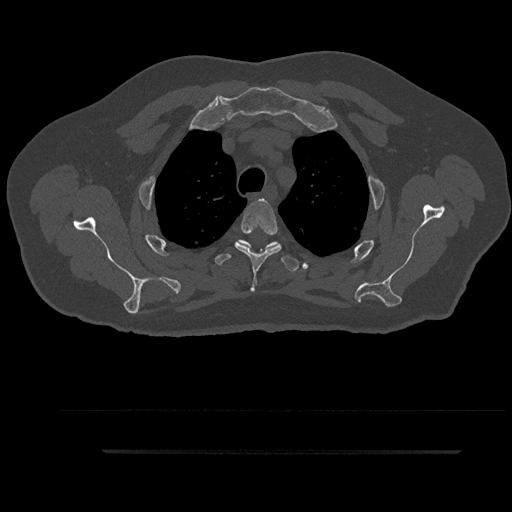
CT including the spine, one axial slice; slice 707 of 797 in the series (ordered by position); 120 kVp; bone window (W 1800 / L 400 HU); 512 × 512 image matrix, field of view 432 × 432 mm. Male patient, age 63 years. Case-level facts recorded for this patient, not image findings: primary cancer: renal; vertebrae with lytic lesions (as recorded): T8.
Annotated regions visible in this slice (semi-automatically segmented with operator editing):
- T3 vertebra: bounding box (x1, y1, x2, y2) in pixels: (235, 199, 281, 292)
- T4 vertebra: (215, 240, 299, 272)